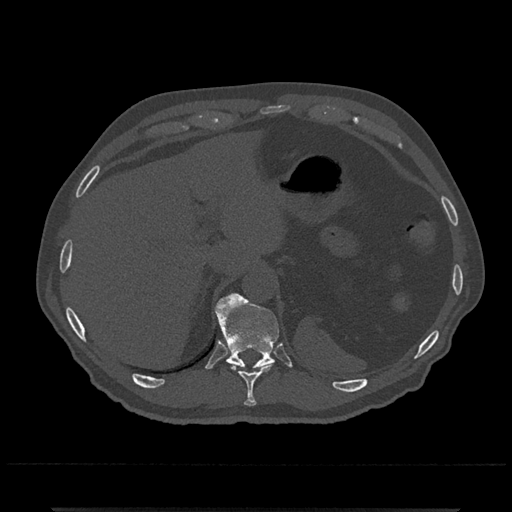
CT including the spine, one axial slice; slice 522 of 797 in the series (ordered by position); reconstruction kernel Br40s/3; 120 kVp; bone window (W 1800 / L 400 HU); 0.5 mm slice thickness; 512 × 512 image matrix, field of view 393 × 393 mm. Patient: male, 67 years. From the clinical record (not read from this slice): primary cancer: prostate.
Structures marked on this image (semi-automatic segmentation, software-assisted and operator-edited):
- T10 vertebra: bounding box [x1, y1, x2, y2] px = [239, 367, 269, 407]
- T11 vertebra: [215, 293, 279, 368]